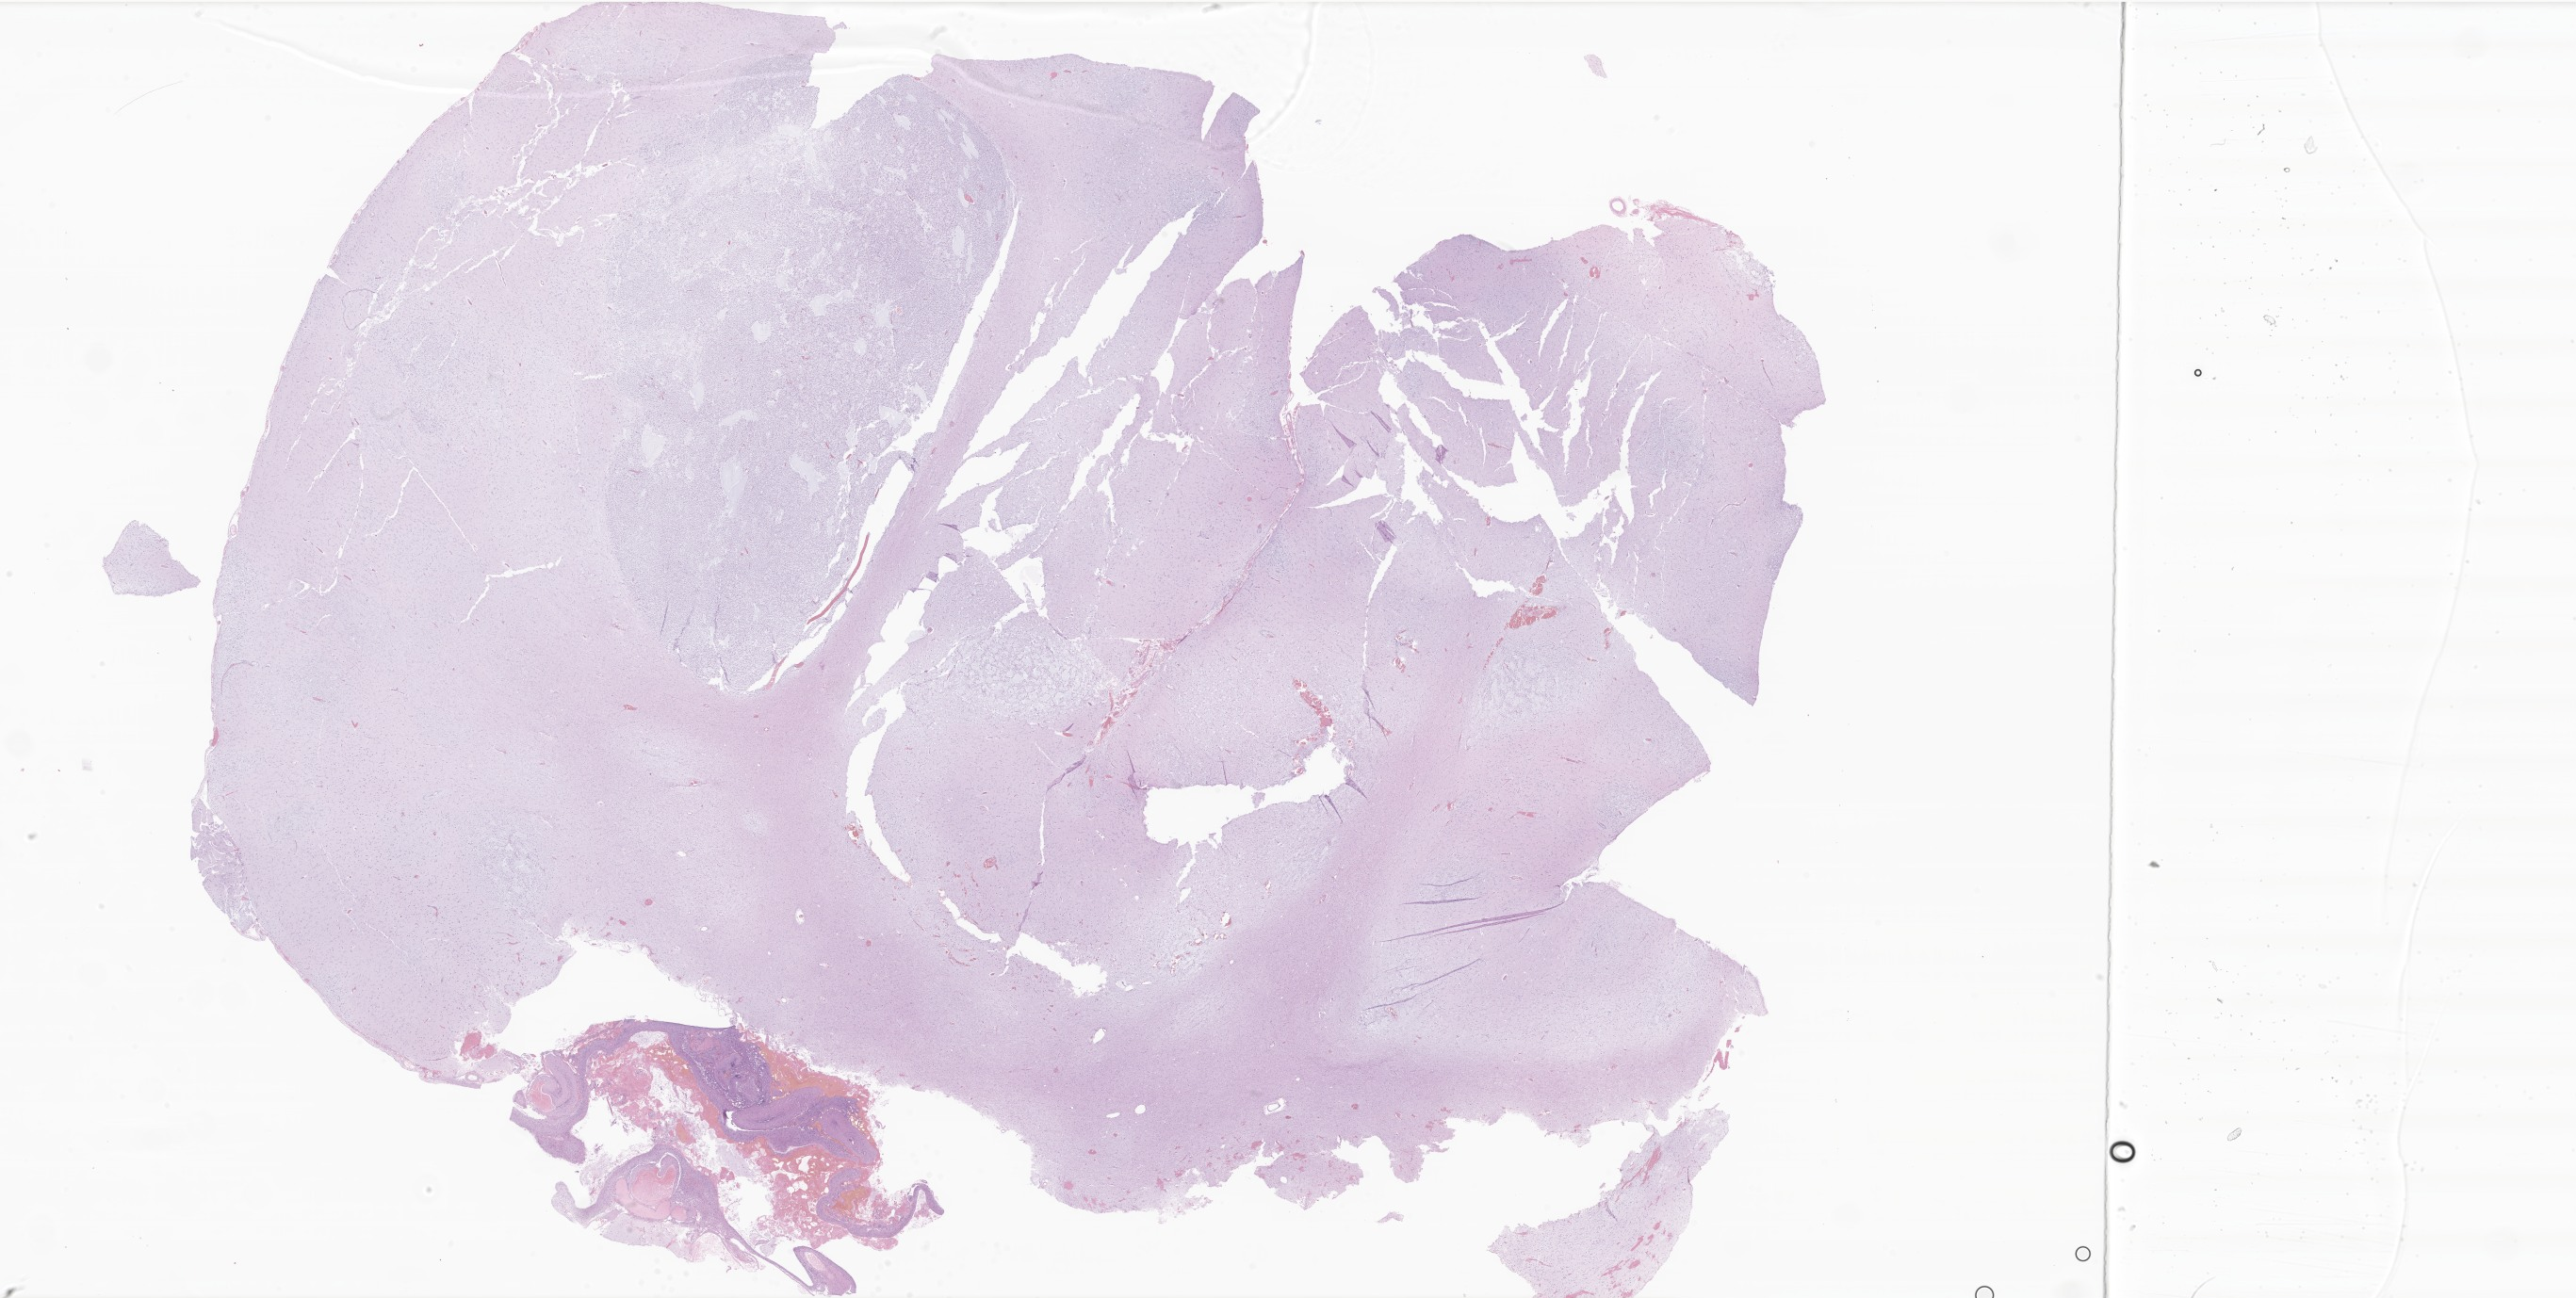
Hematoxylin and eosin (H&E) whole-slide image of tumor tissue from the temporal lobe, whole scanned area (about 46.1 x 23.2 mm) shown as a low-resolution overview, FFPE section. Patient: female, age 219 months (18 years 3 months).
Diagnosis (ICD-O-3 morphology term): Glioma, malignant.